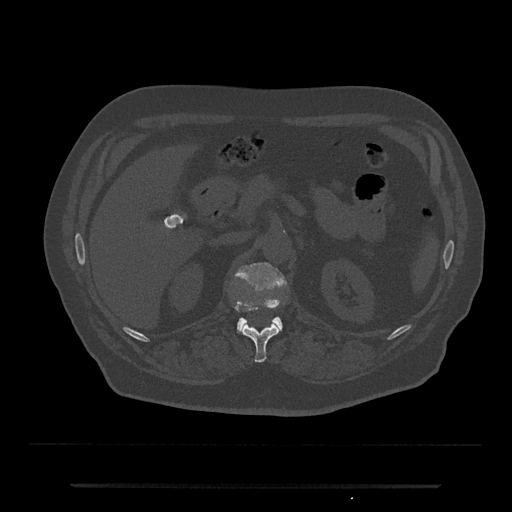
CT including the spine, one axial slice. Slice 569 of 797 in the series (ordered by position). 120 kVp. Bone window (W 1800 / L 400 HU). 0.5 mm slice thickness. 512 × 512 image matrix. Male patient, age 80 years. From the clinical record (not read from this slice): primary cancer: prostate; vertebrae with lytic lesions (as recorded): L1, T11.
Annotated regions visible in this slice (semi-automatic segmentation, software-assisted and operator-edited):
- L1 vertebra: bounding box <234,262,287,333> (left, top, right, bottom; pixels)
- T12 vertebra: <236,308,281,363>